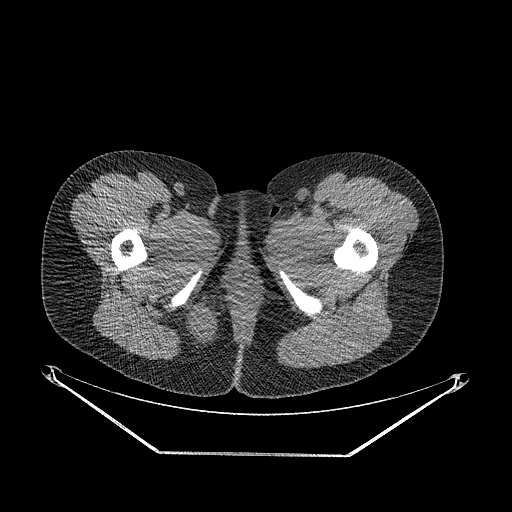
CT of an extremity soft-tissue mass (from a PET/CT study), one axial slice. 120 kVp. Soft-tissue window (W 400 / L 40 HU). 512 × 512 image matrix. Female patient. Case-level facts recorded for this patient, not image findings: histological type: epithelioid sarcoma; grade: intermediate; site of the primary tumour: right buttock.
Annotated regions visible in this slice (expert contour drawn on MRI and transferred to this co-registered scan by the dataset authors):
- gross tumour volume including surrounding oedema: bounding box <176,297,223,353> (left, top, right, bottom; pixels)
- gross tumour volume (mass): <180,306,216,348>